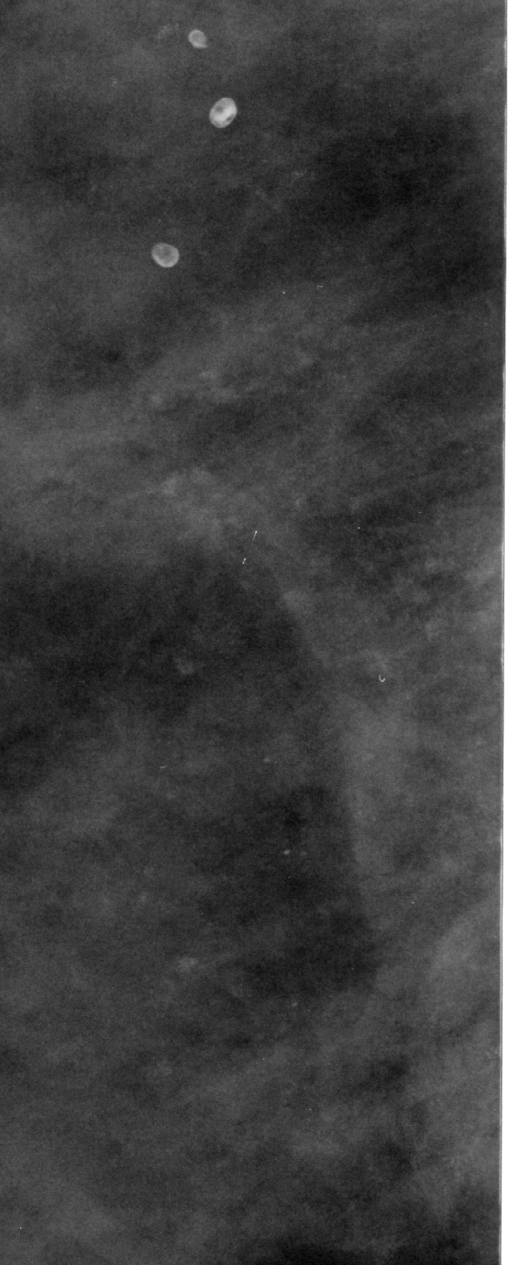
Crop from a digitized film mammogram around one marked abnormality; right breast; CC view.
Finding: calcifications, morphology punctate / amorphous, distribution regional; BI-RADS assessment category 4; pathology result (as recorded, not read from the image): benign.